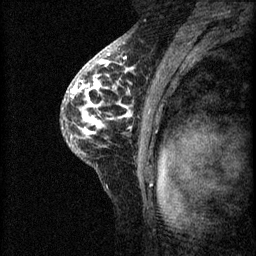
Breast MRI (dynamic contrast-enhanced), one sagittal slice. 3 images stored at this slice position (order not interpretable as contrast timing). 1.5 T. TE 4.2 ms, TR 8.2 ms. 2 mm slice thickness. 256 × 256 image matrix, field of view 180 × 180 mm. Patient: female, 41 years.
Outlined on this slice (semi-automatic segmentation, software-assisted and operator-edited):
- analysis volume of interest (the breast-tissue region the enhancement analysis was run in; not a lesion): bounding box <61,62,158,175> (left, top, right, bottom; pixels)
- tumour enhancement mask (voxels above the 70 % enhancement threshold inside the analysis volume of interest): <70,62,133,137>